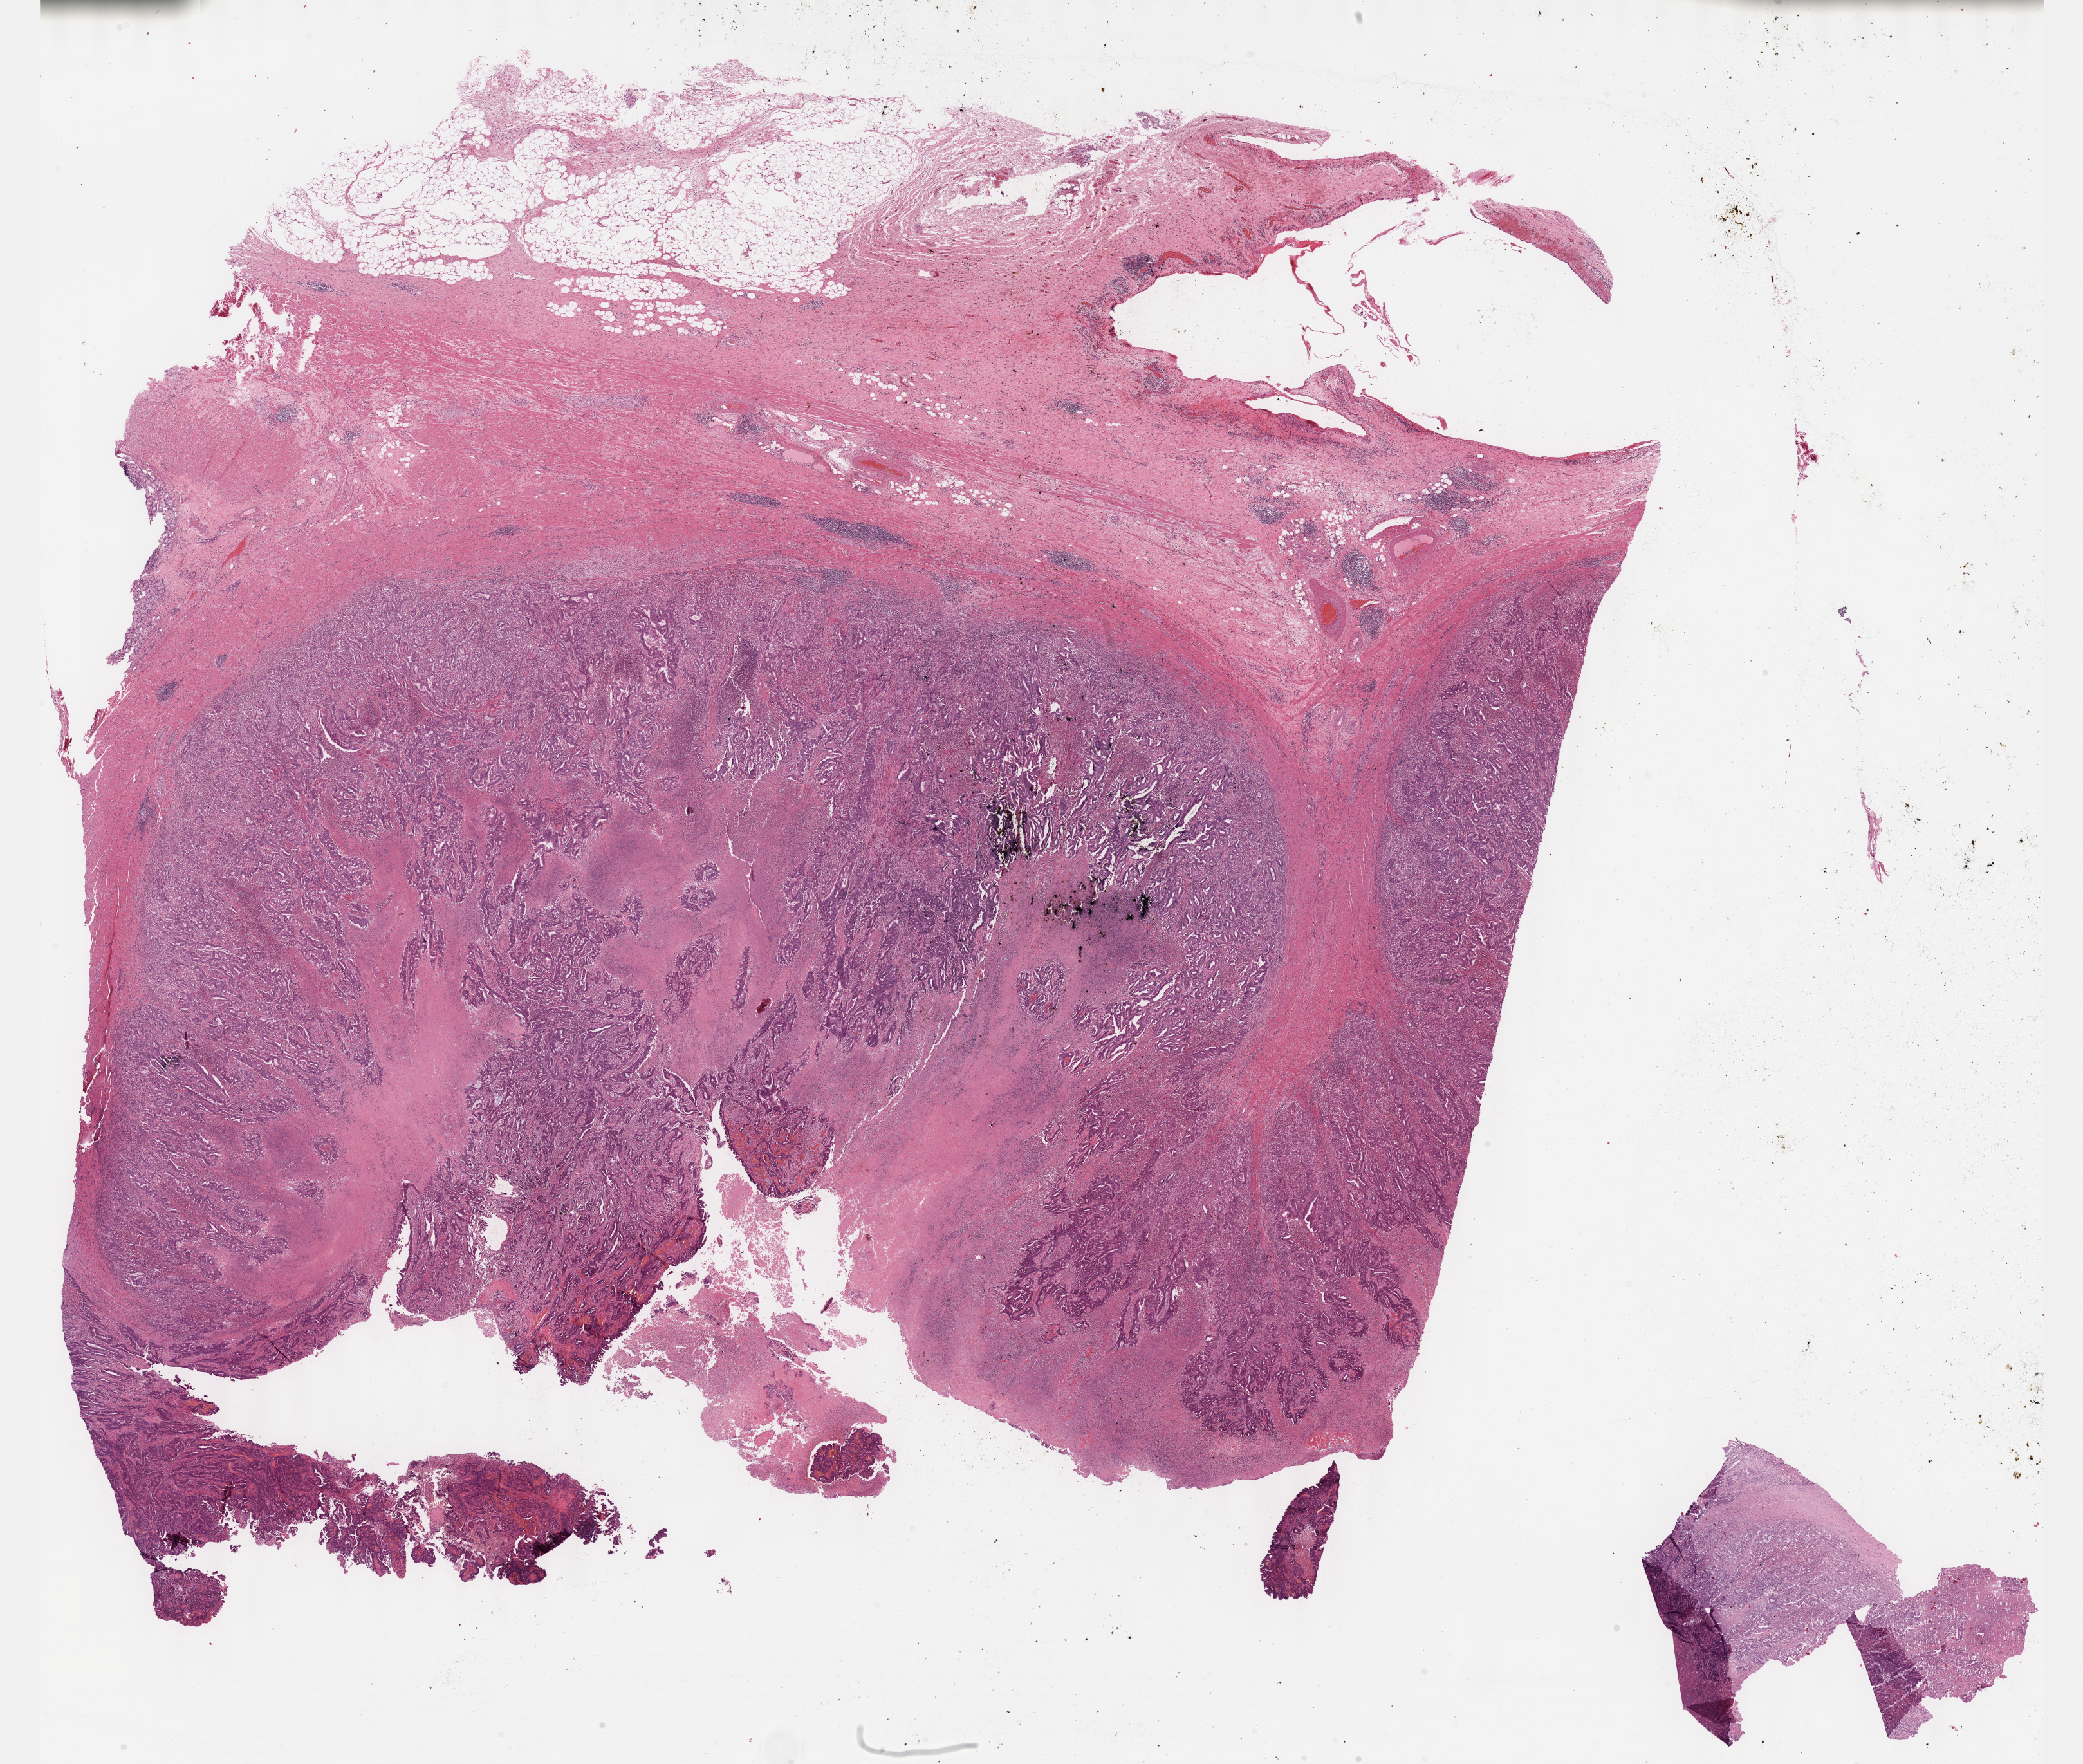
Digitized H&E tissue section (whole slide), whole scanned area (about 26.2 x 22.1 mm) shown as a low-resolution overview. Formalin-fixed paraffin-embedded (FFPE) diagnostic section. Primary tumour sample from the stomach. Female, age 65 years at initial diagnosis. Histologic grade: G2 (moderately differentiated).
* AJCC pathologic stage: II
* pathologic diagnosis: Papillary adenocarcinoma, NOS (gastric antrum)